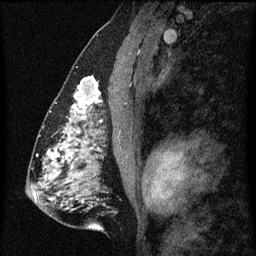
Breast MRI (dynamic contrast-enhanced), one sagittal slice. Slice 34 of 60 in the series (ordered by position). Dynamic contrast-enhanced series, image 2 of 3 at this slice position (ordered by acquisition). 1.5 T. TE 4.2 ms, TR 8 ms. 2 mm slice thickness. 256 × 256 image matrix. Patient: female, 51 years.
Outlined on this slice (semi-automatic segmentation, software-assisted and operator-edited):
- analysis volume of interest (the breast-tissue region the enhancement analysis was run in; not a lesion): bounding box [x1, y1, x2, y2] px = [62, 76, 102, 129]
- tumour enhancement mask (voxels above the 70 % enhancement threshold inside the analysis volume of interest): [69, 76, 102, 123]